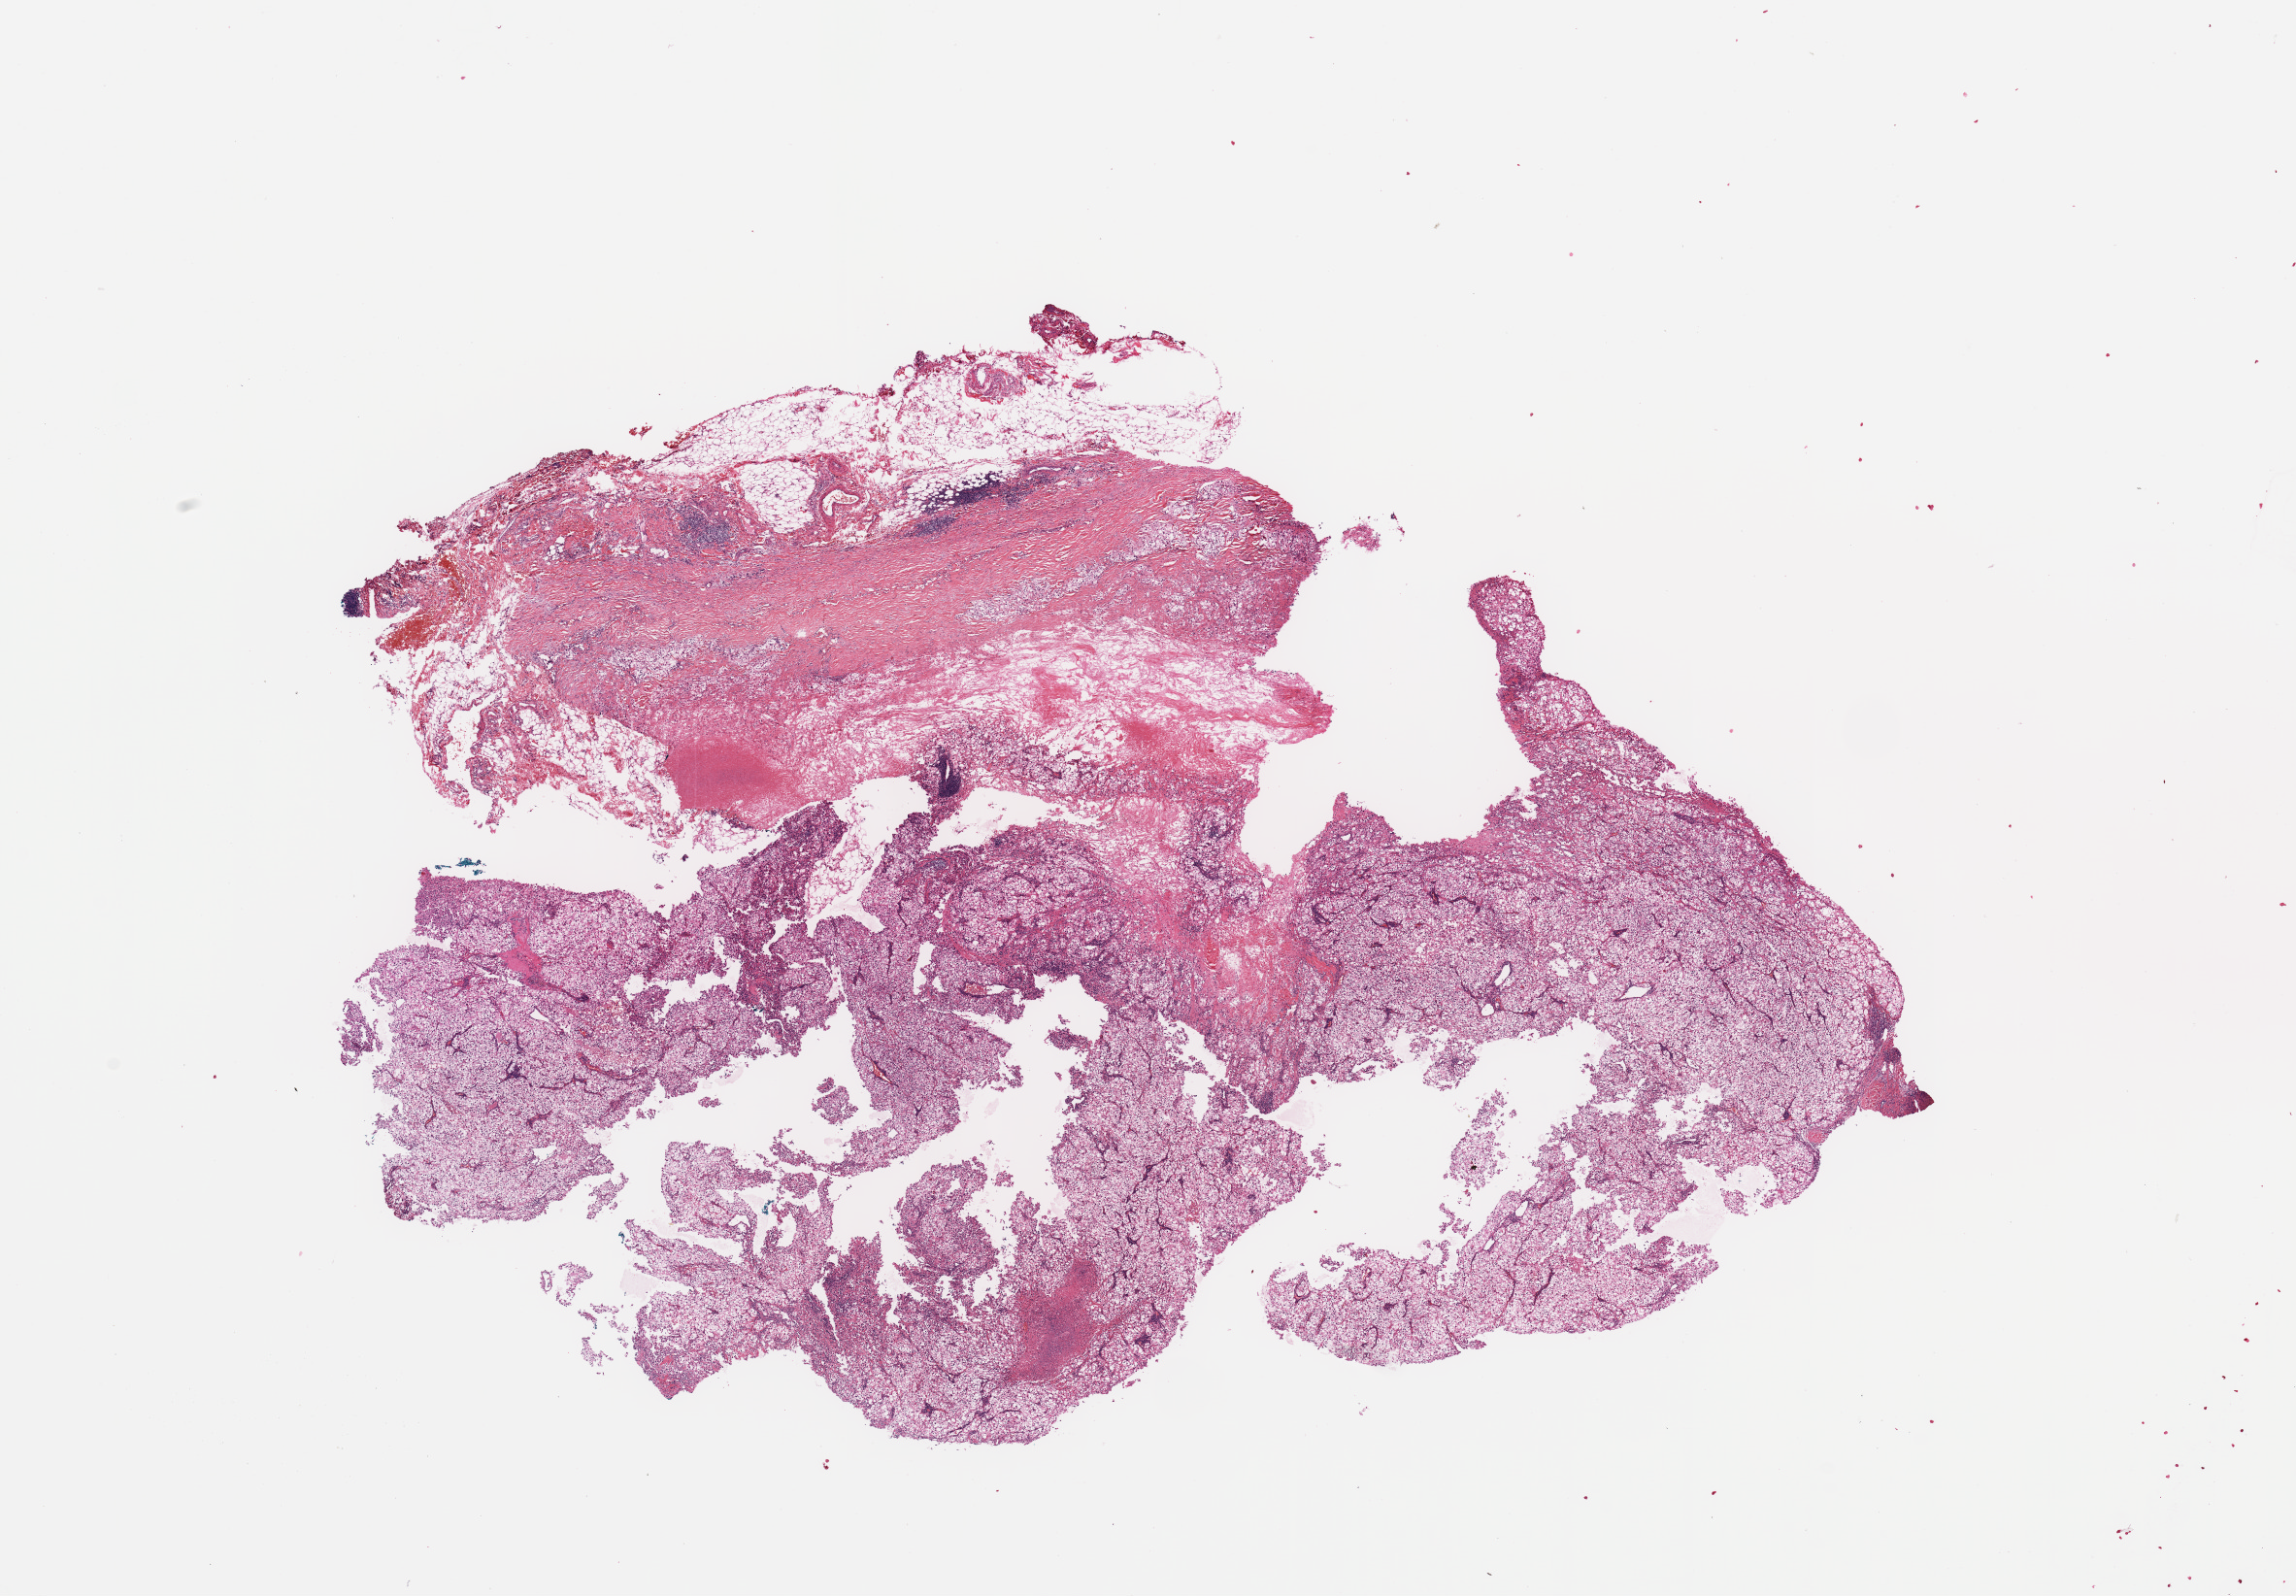
H&E-stained whole-slide image, shown as a low-resolution overview of the whole scanned area (about 18.7 x 13.0 mm); tumour tissue sample, sampled site: kidney. Male, 63 y/o. Histologic grade: G2 (moderately differentiated). Slide review estimates, as recorded: tumour nuclei 80%, necrosis 5%.
- diagnosis: Renal cell carcinoma, NOS
- AJCC pathologic stage: I
- primary tumour site (as recorded): middle